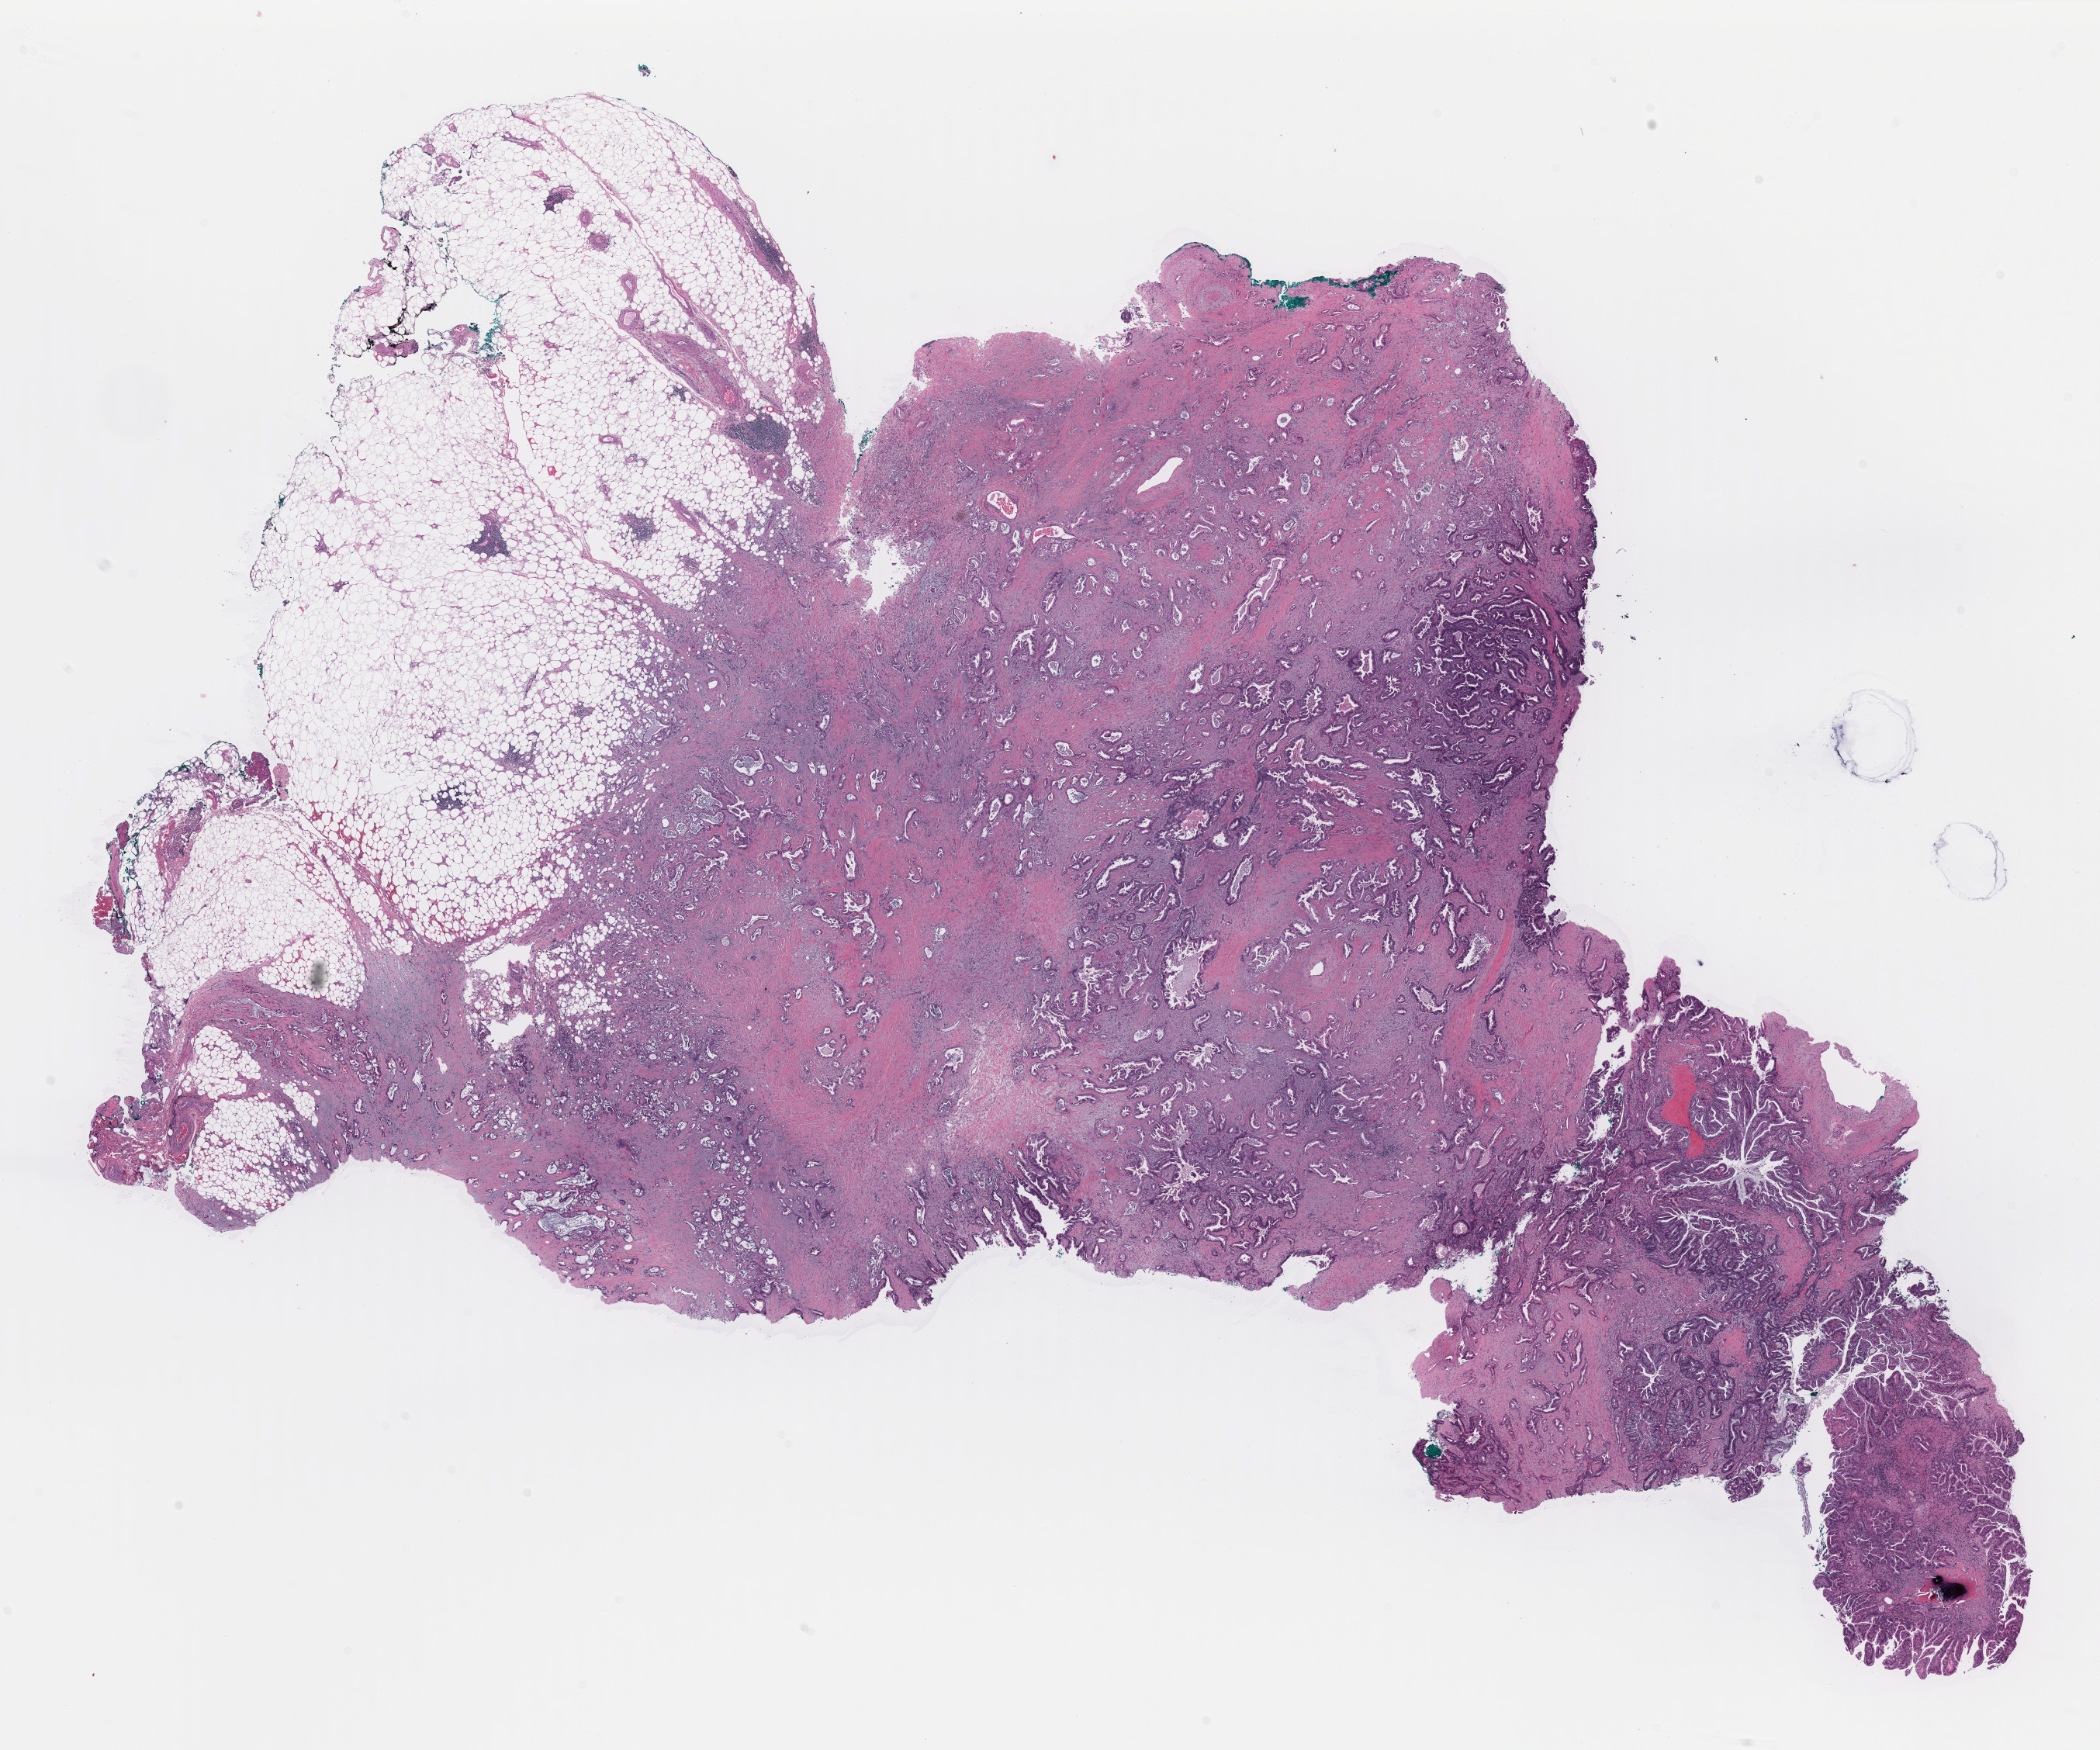
H&E whole-slide image, whole scanned area (about 21.4 x 17.8 mm, slide scanned at 40x) shown as a low-resolution overview. Formalin-fixed paraffin-embedded (FFPE) diagnostic section. Primary tumour sample from the pancreas. Patient: male, age at initial diagnosis 76 years. Histologic grade: G2 (moderately differentiated).
Histologic diagnosis: Infiltrating duct carcinoma, NOS (head of pancreas). Lymph nodes positive (case pathology): 0 of 13 examined. AJCC pathologic stage: IIA (7th edition).